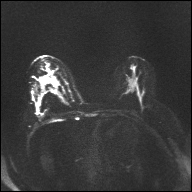
Breast MRI, one axial slice; position 18 of 32 along the scan axis; diffusion-weighted series; image 2 of 4 stored at this slice position (different b-values; order by instance number); 1.5 T; 4 mm slice thickness; 192 × 192 image matrix, field of view 360 × 360 mm. Female patient.
Annotated regions visible in this slice (manually delineated by an expert):
- tumour on diffusion-weighted imaging: bounding box <47,69,50,74> (left, top, right, bottom; pixels)